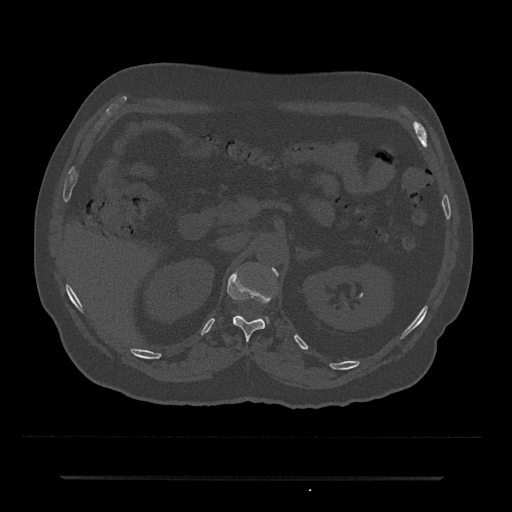
CT including the spine, one axial slice; slice 116 of 797 in the series (ordered by position); 120 kVp; bone window (W 1800 / L 400 HU); 0.5 mm slice thickness; 512 × 512 image matrix. Male patient, age 69 years. From the clinical record (not read from this slice): primary cancer: prostate.
Annotated regions visible in this slice (semi-automatically segmented with operator editing):
- L1 vertebra: bounding box <262,269,275,323> (left, top, right, bottom; pixels)
- T12 vertebra: <227,267,278,340>